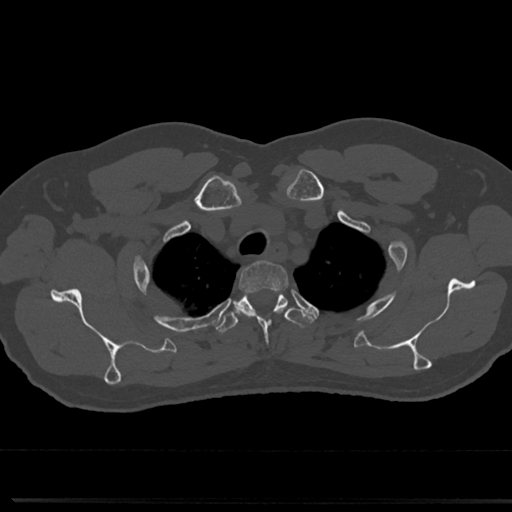
CT including the spine, one axial slice; position 612 of 817 along the scan axis; reconstruction kernel Br40s/3; bone window (W 1800 / L 400 HU); 0.5 mm slice thickness; 512 × 512 image matrix. Patient: male, 61 years. From the clinical record (not read from this slice): primary cancer: prostate.
Outlined on this slice (semi-automatically segmented with operator editing):
- T2 vertebra: bounding box <239,262,289,289> (left, top, right, bottom; pixels)
- T3 vertebra: <215,289,311,334>